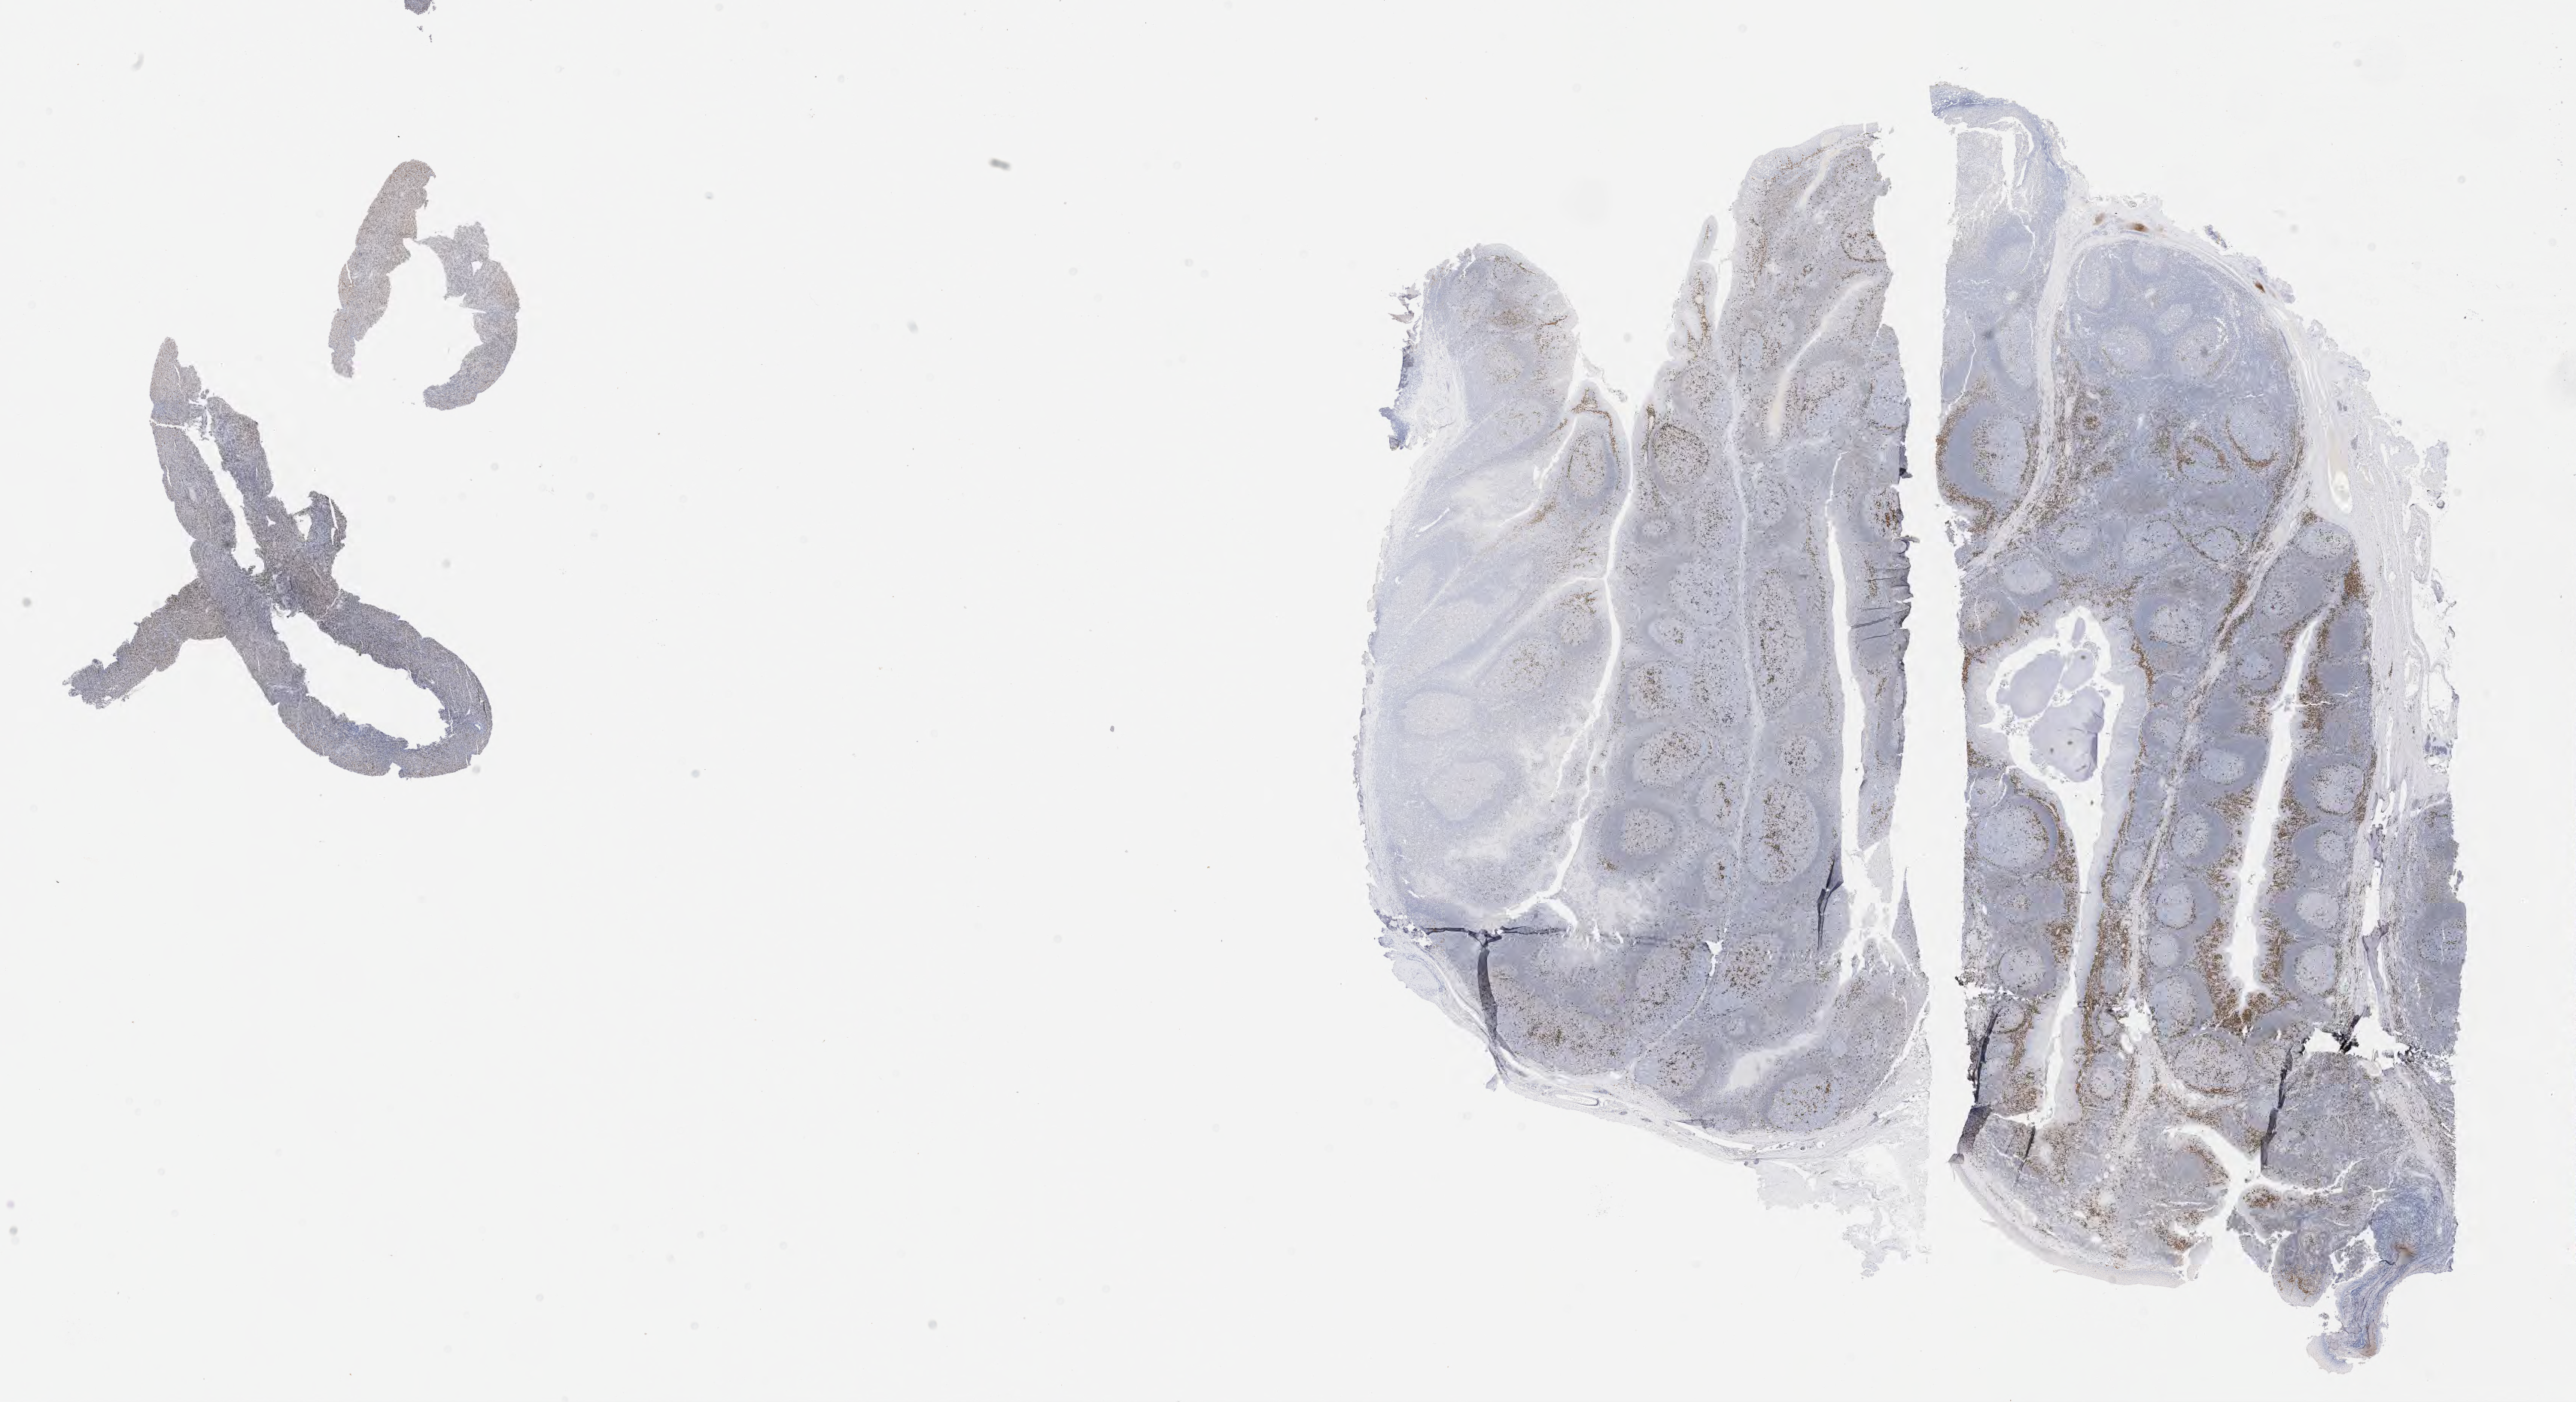
Immunohistochemistry (IHC) whole-slide image stained for IRF4/MUM1, whole scanned area (about 27.7 x 15.1 mm) shown as a low-resolution overview. Patient male; aged 52.
* specimen: tumor tissue; anatomic site: liver